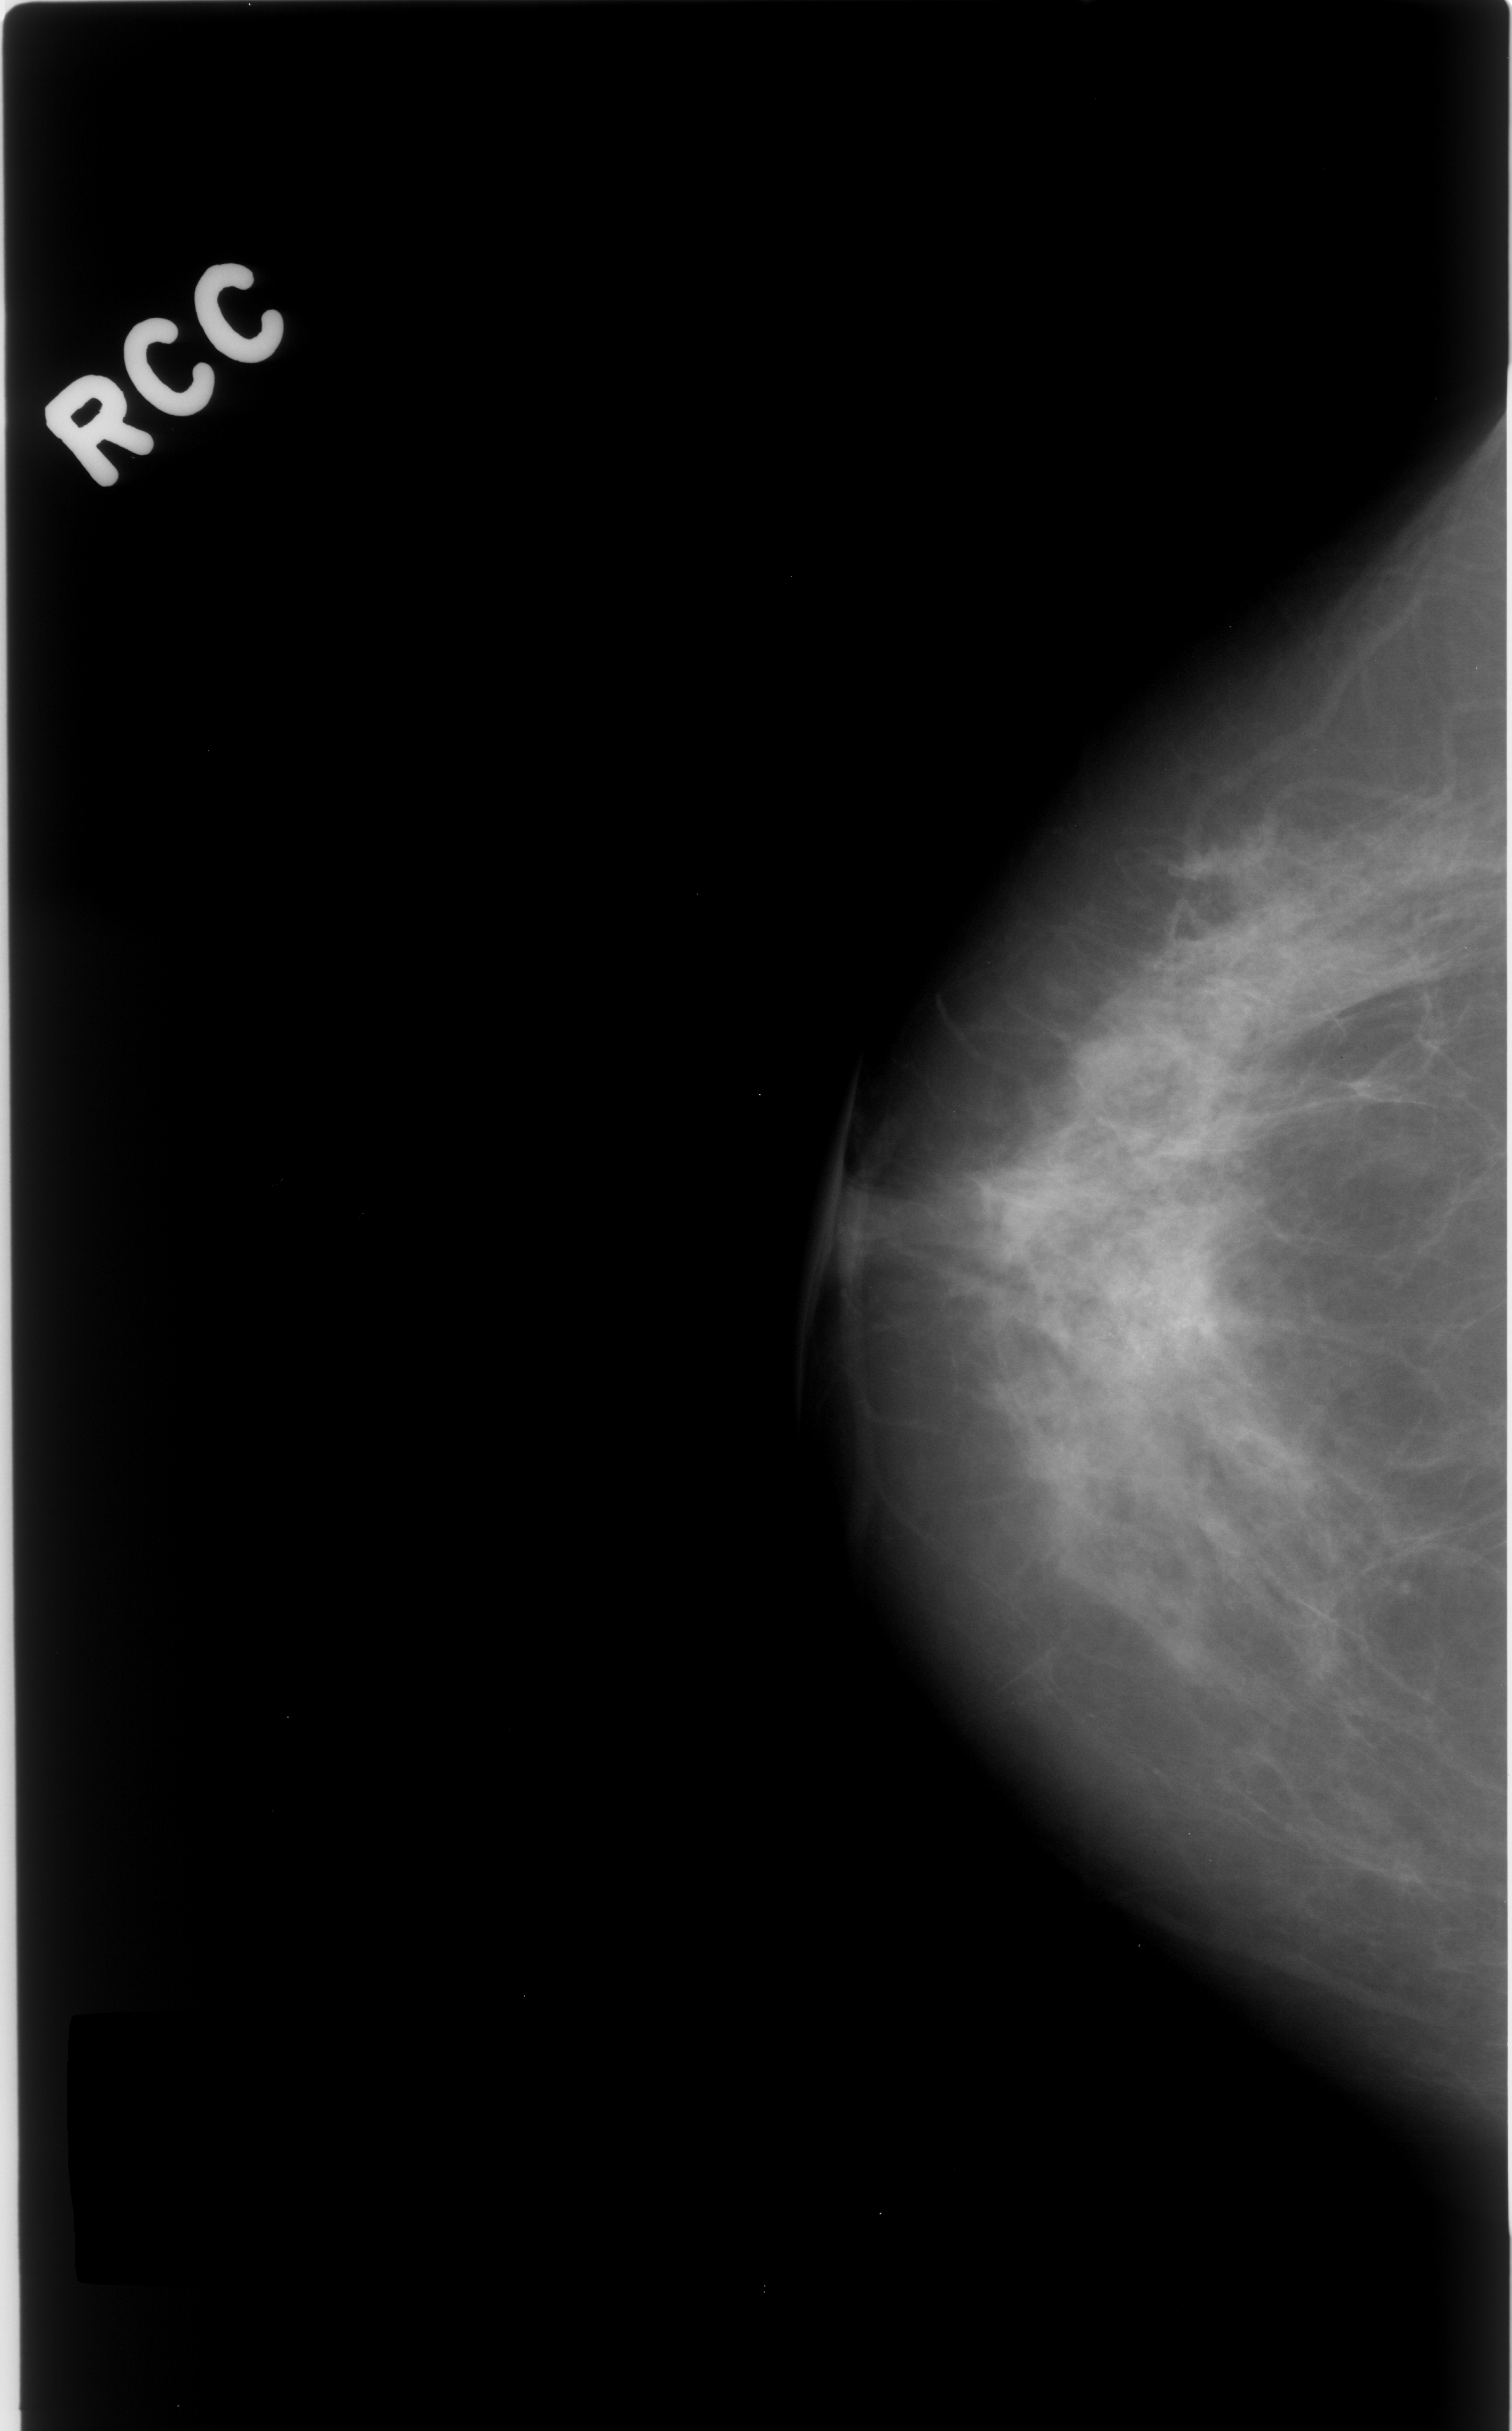
Scanned film-screen mammogram, right breast, CC view, breast composition: scattered fibroglandular densities (BI-RADS density category 2 of 4).
Finding: calcifications, morphology amorphous, distribution clustered; BI-RADS assessment category 4; pathology (as recorded): benign.